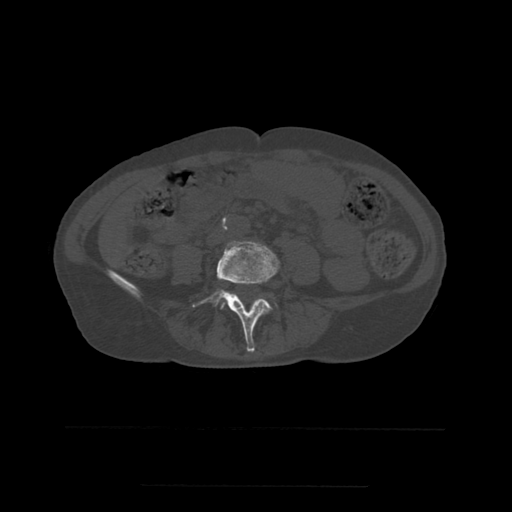
CT including the spine, one axial slice. Slice 163 of 544 in the series (ordered by position). Bone window (W 1800 / L 400 HU). 512 × 512 image matrix. Patient age 58 years. From the clinical record (not read from this slice): primary cancer: lung.
Outlined on this slice (semi-automatically segmented with operator editing):
- L4 vertebra: bounding box (x1, y1, x2, y2) in pixels: (193, 242, 279, 353)
- L5 vertebra: (222, 291, 239, 309)